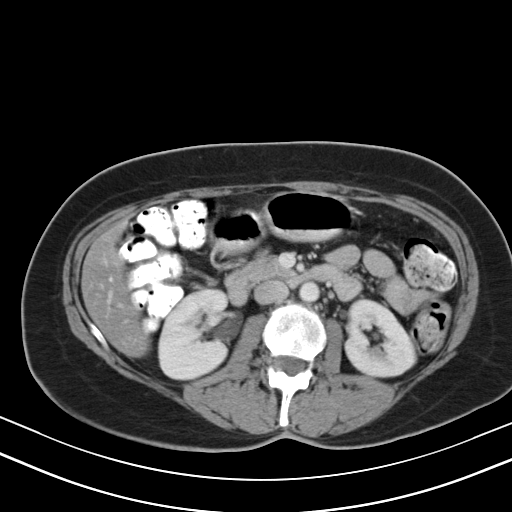
Contrast-enhanced abdominal CT, one axial slice; position 19 of 47 along the scan axis; intravenous contrast given; soft-tissue window (W 400 / L 40 HU); 5 mm slice thickness; 512 × 512 image matrix. Female patient. From the clinical record (not read from this slice): diagnosis: colorectal cancer liver metastases, imaged before liver resection; multiple liver metastases: no; largest metastasis: 3.5 cm.
Annotated regions visible in this slice (expert manual segmentation):
- liver: bounding box (x1, y1, x2, y2) in pixels: (83, 231, 148, 355)
- planned liver remnant (the part of the liver to remain after resection): (83, 231, 148, 355)